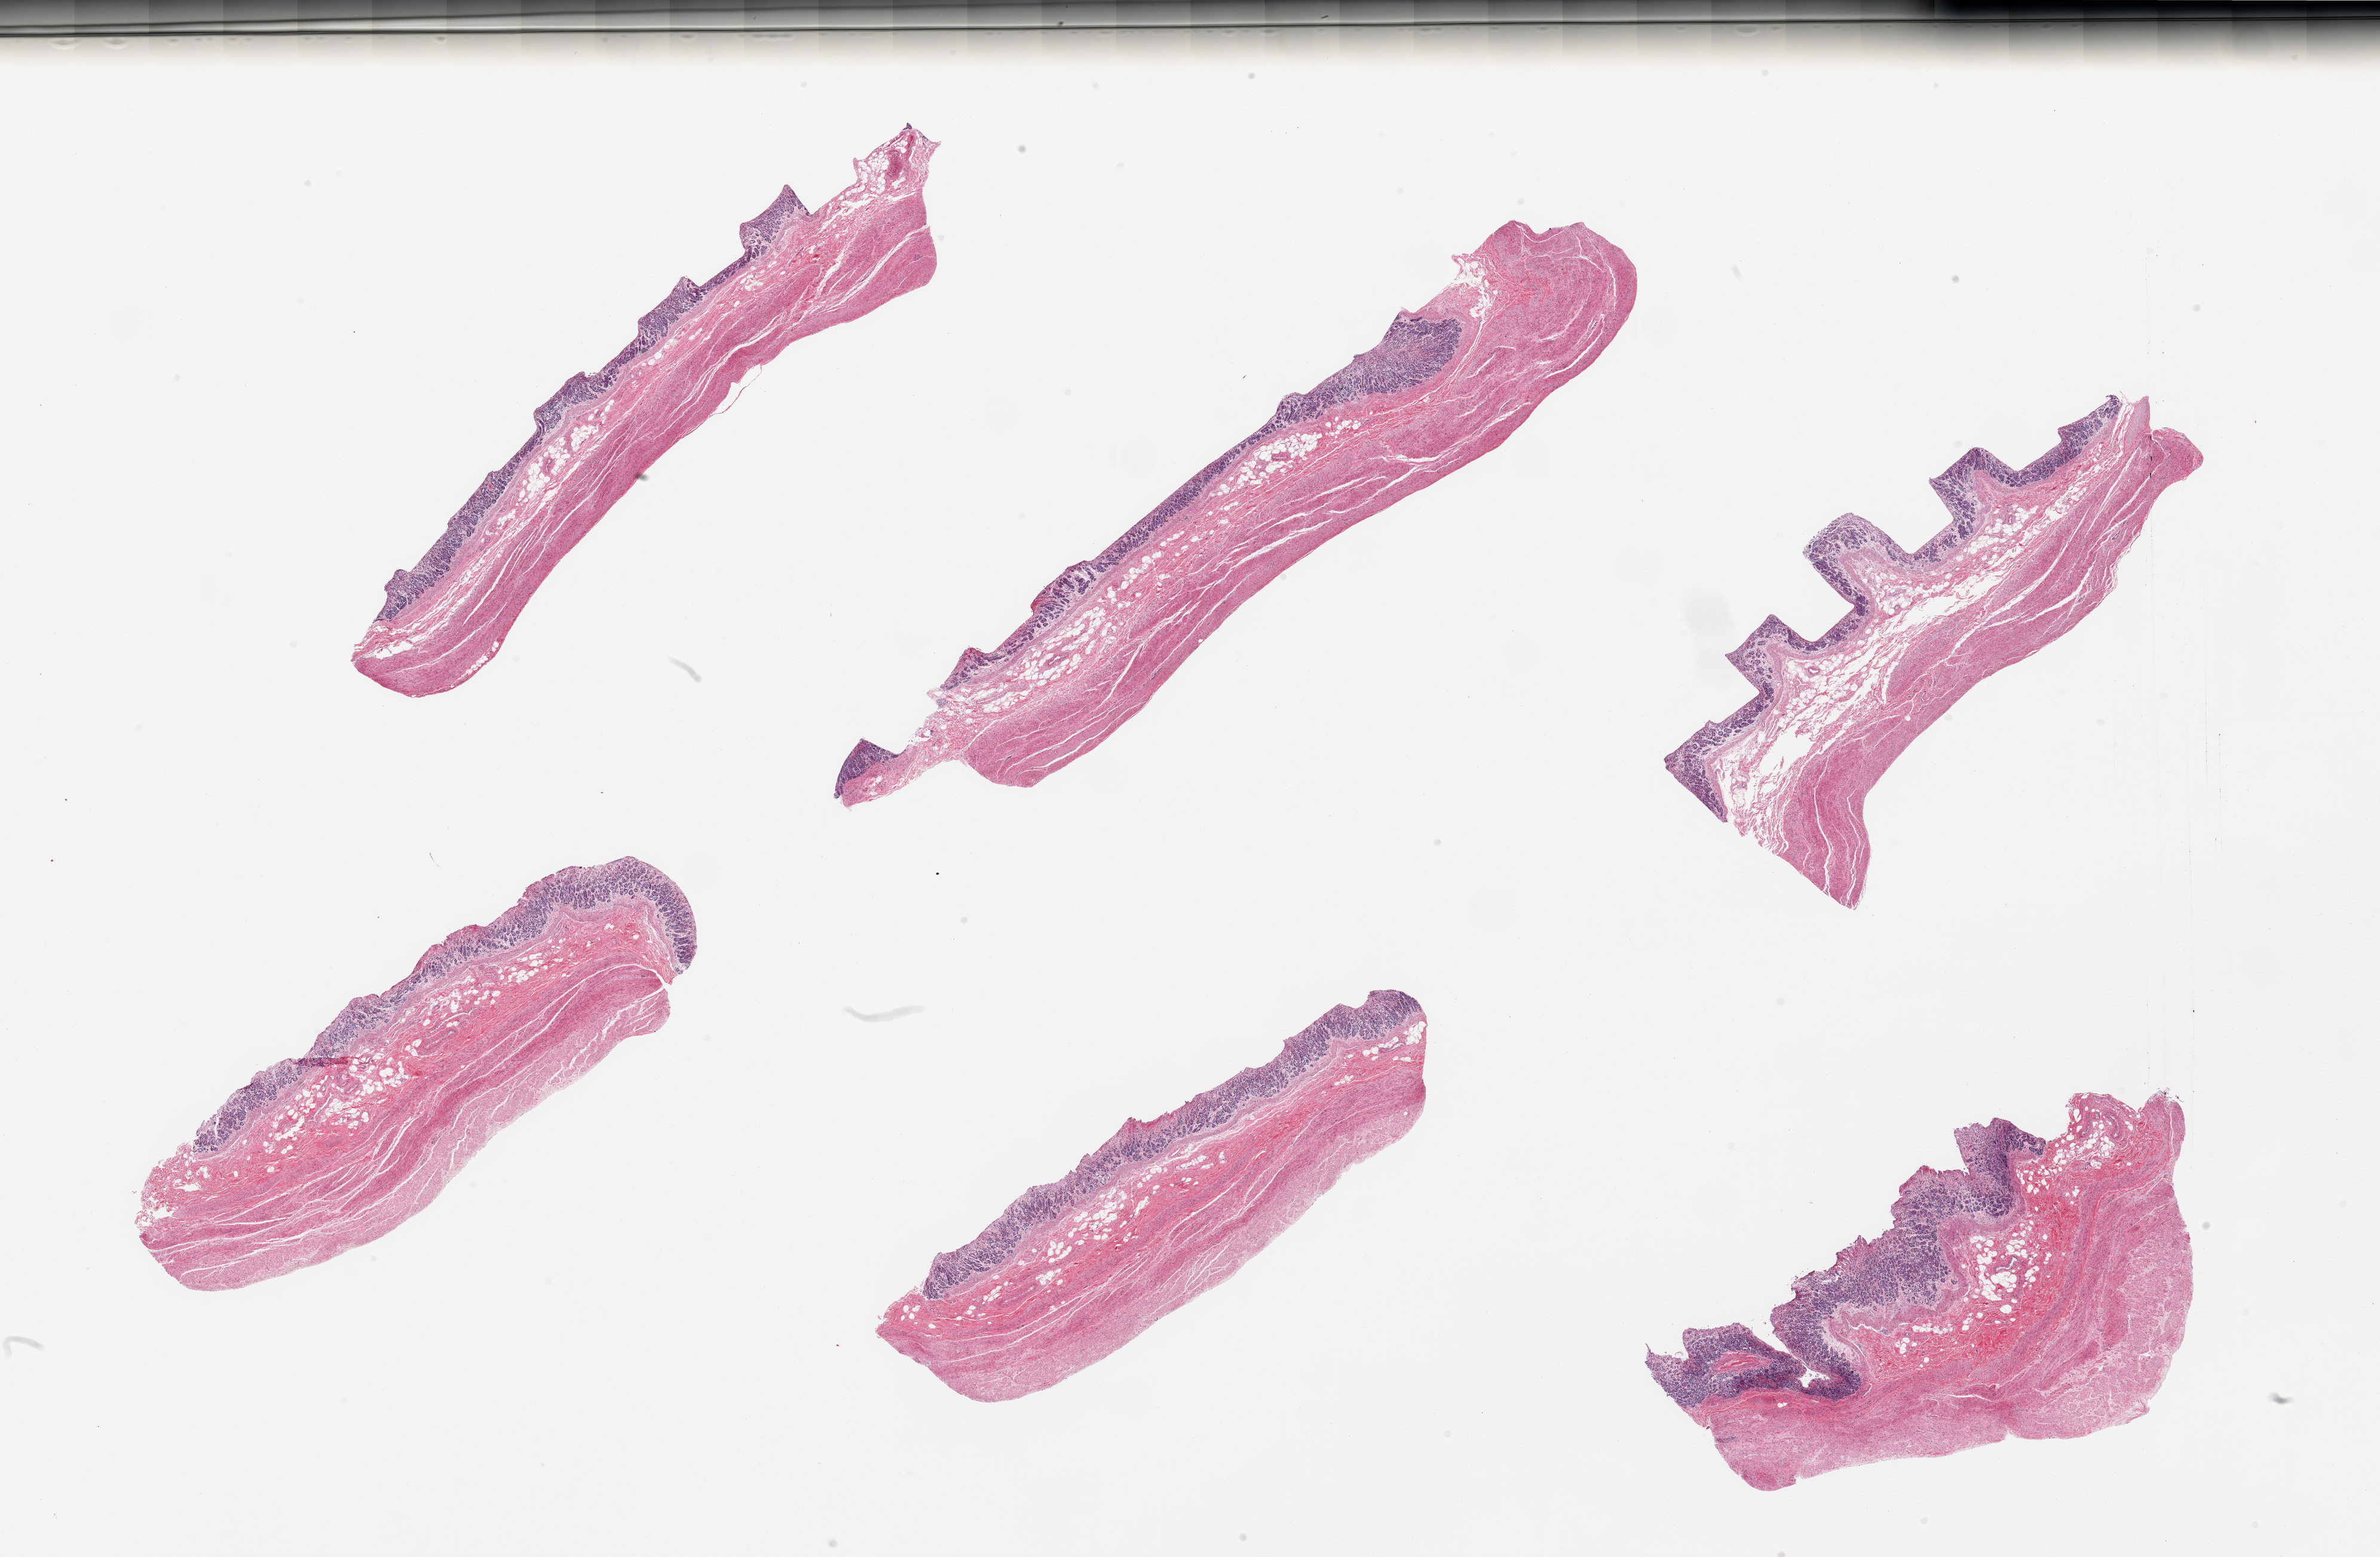
Hematoxylin and eosin (H&E) whole-slide image, brightfield, shown as a low-resolution overview of the whole scanned area (about 31.5 x 20.6 mm, acquisition: 20x scan); PAXgene-fixed, paraffin-embedded tissue; sampled site (target tissue): stomach; donor tissue sample. Donor: male.
Pathologist's review note for this sample: 6 pieces, mucosa up to ~0.6mm,~15% thickness, but moderate-advanced autolysis.